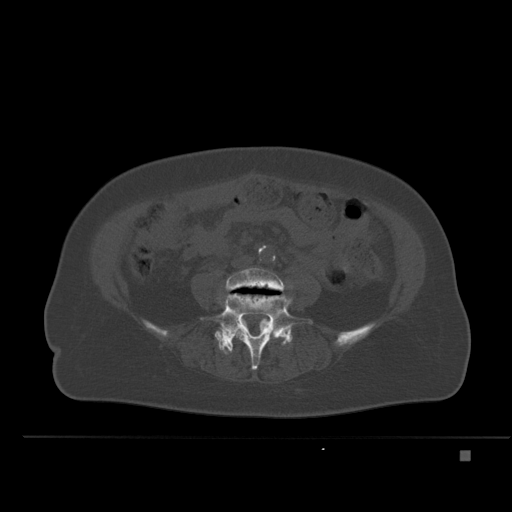
CT including the spine, one axial slice. Position 167 of 477 along the scan axis. Bone window (W 1800 / L 400 HU). 512 × 512 image matrix, field of view 422 × 422 mm. Female patient, age 74 years. Case-level facts recorded for this patient, not image findings: primary cancer: colon.
Outlined on this slice (semi-automatically segmented with operator editing):
- L4 vertebra: bounding box (x1, y1, x2, y2) in pixels: (225, 267, 289, 336)
- L5 vertebra: (218, 294, 312, 370)